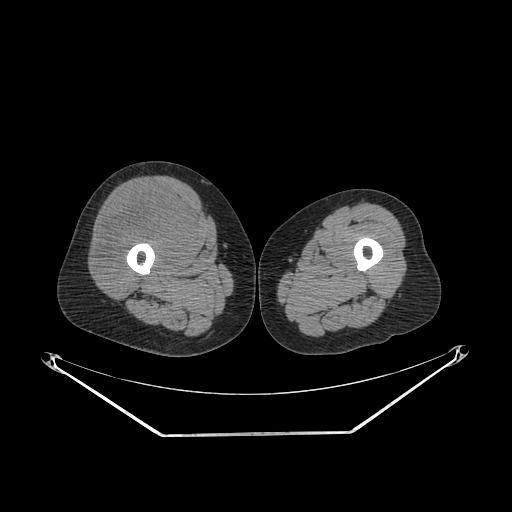
CT of an extremity soft-tissue mass (from a PET/CT study), one axial slice; position 240 of 311 along the scan axis; 140 kVp; soft-tissue window (W 400 / L 40 HU); 3.75 mm slice thickness; 512 × 512 image matrix, field of view 500 × 500 mm. Female patient. Case-level facts recorded for this patient, not image findings: histological type: pleiomorphic undifferentiated sarcoma; grade: high; site of the primary tumour: right quadricep.
Annotated regions visible in this slice (expert contour drawn on MRI and transferred to this co-registered scan by the dataset authors):
- tumour plus oedema (research contour): box from (x=98, y=192) to (x=188, y=282) px
- tumour (research contour): (x=98, y=192)–(x=188, y=282)